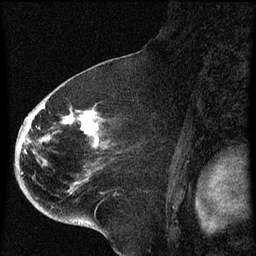
Breast MRI (dynamic contrast-enhanced), one sagittal slice. Slice 39 of 60 in the series (ordered by position). Dynamic contrast-enhanced series, image 2 of 4 at this slice position (ordered by acquisition). 1.5 T. TE 4.2 ms, TR 8 ms. 2 mm slice thickness. 256 × 256 image matrix, field of view 180 × 180 mm. Patient: female, 71 years.
Structures marked on this image (semi-automatic segmentation, software-assisted and operator-edited):
- analysis volume of interest (the breast-tissue region the enhancement analysis was run in; not a lesion): box from (x=32, y=86) to (x=140, y=205) px
- tumour enhancement mask (voxels above the 70 % enhancement threshold inside the analysis volume of interest): (x=32, y=106)–(x=99, y=149)